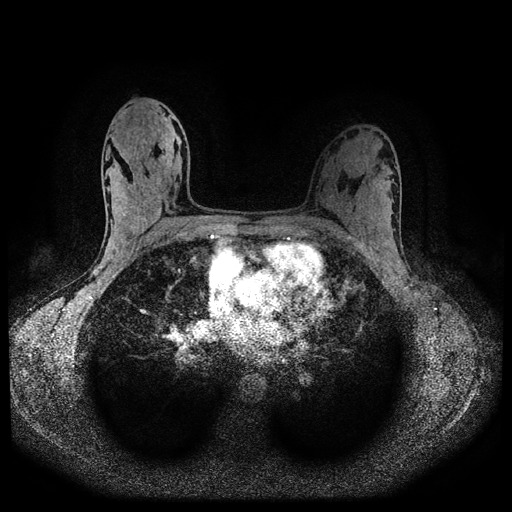
Breast MRI (dynamic contrast-enhanced, multi-phase), one axial slice; slice 61 of 116 in the series (ordered by position); dynamic contrast-enhanced series, time point 2 of 5 at this slice position (early post-contrast); 1.5 T; TE 2.7 ms, TR 5.4 ms; 512 × 512 image matrix. Patient: female, 32 years.
Outlined on this slice (semi-automatically segmented with operator editing):
- breast lesion (labelled benign in the annotation): bounding box (x1, y1, x2, y2) in pixels: (111, 162, 121, 179)